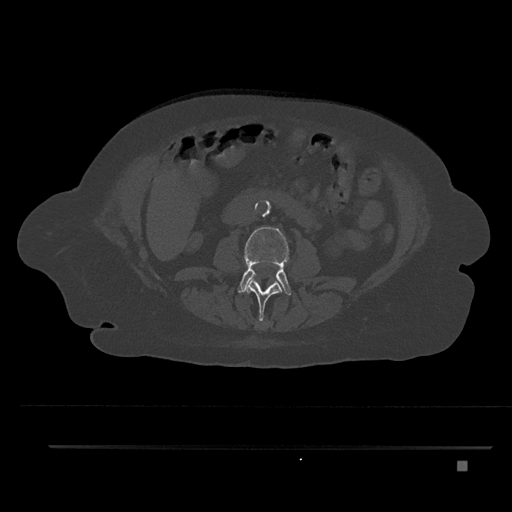
CT including the spine, one axial slice; position 151 of 797 along the scan axis; reconstruction kernel Br40s/3; 120 kVp; bone window (W 1800 / L 400 HU); 0.5 mm slice thickness; 512 × 512 image matrix, field of view 437 × 437 mm. Female patient, age 76 years. From the clinical record (not read from this slice): primary cancer: lung.
Outlined on this slice (semi-automatic segmentation, software-assisted and operator-edited):
- L2 vertebra: bounding box (x1, y1, x2, y2) in pixels: (245, 279, 282, 327)
- L3 vertebra: (237, 227, 292, 295)